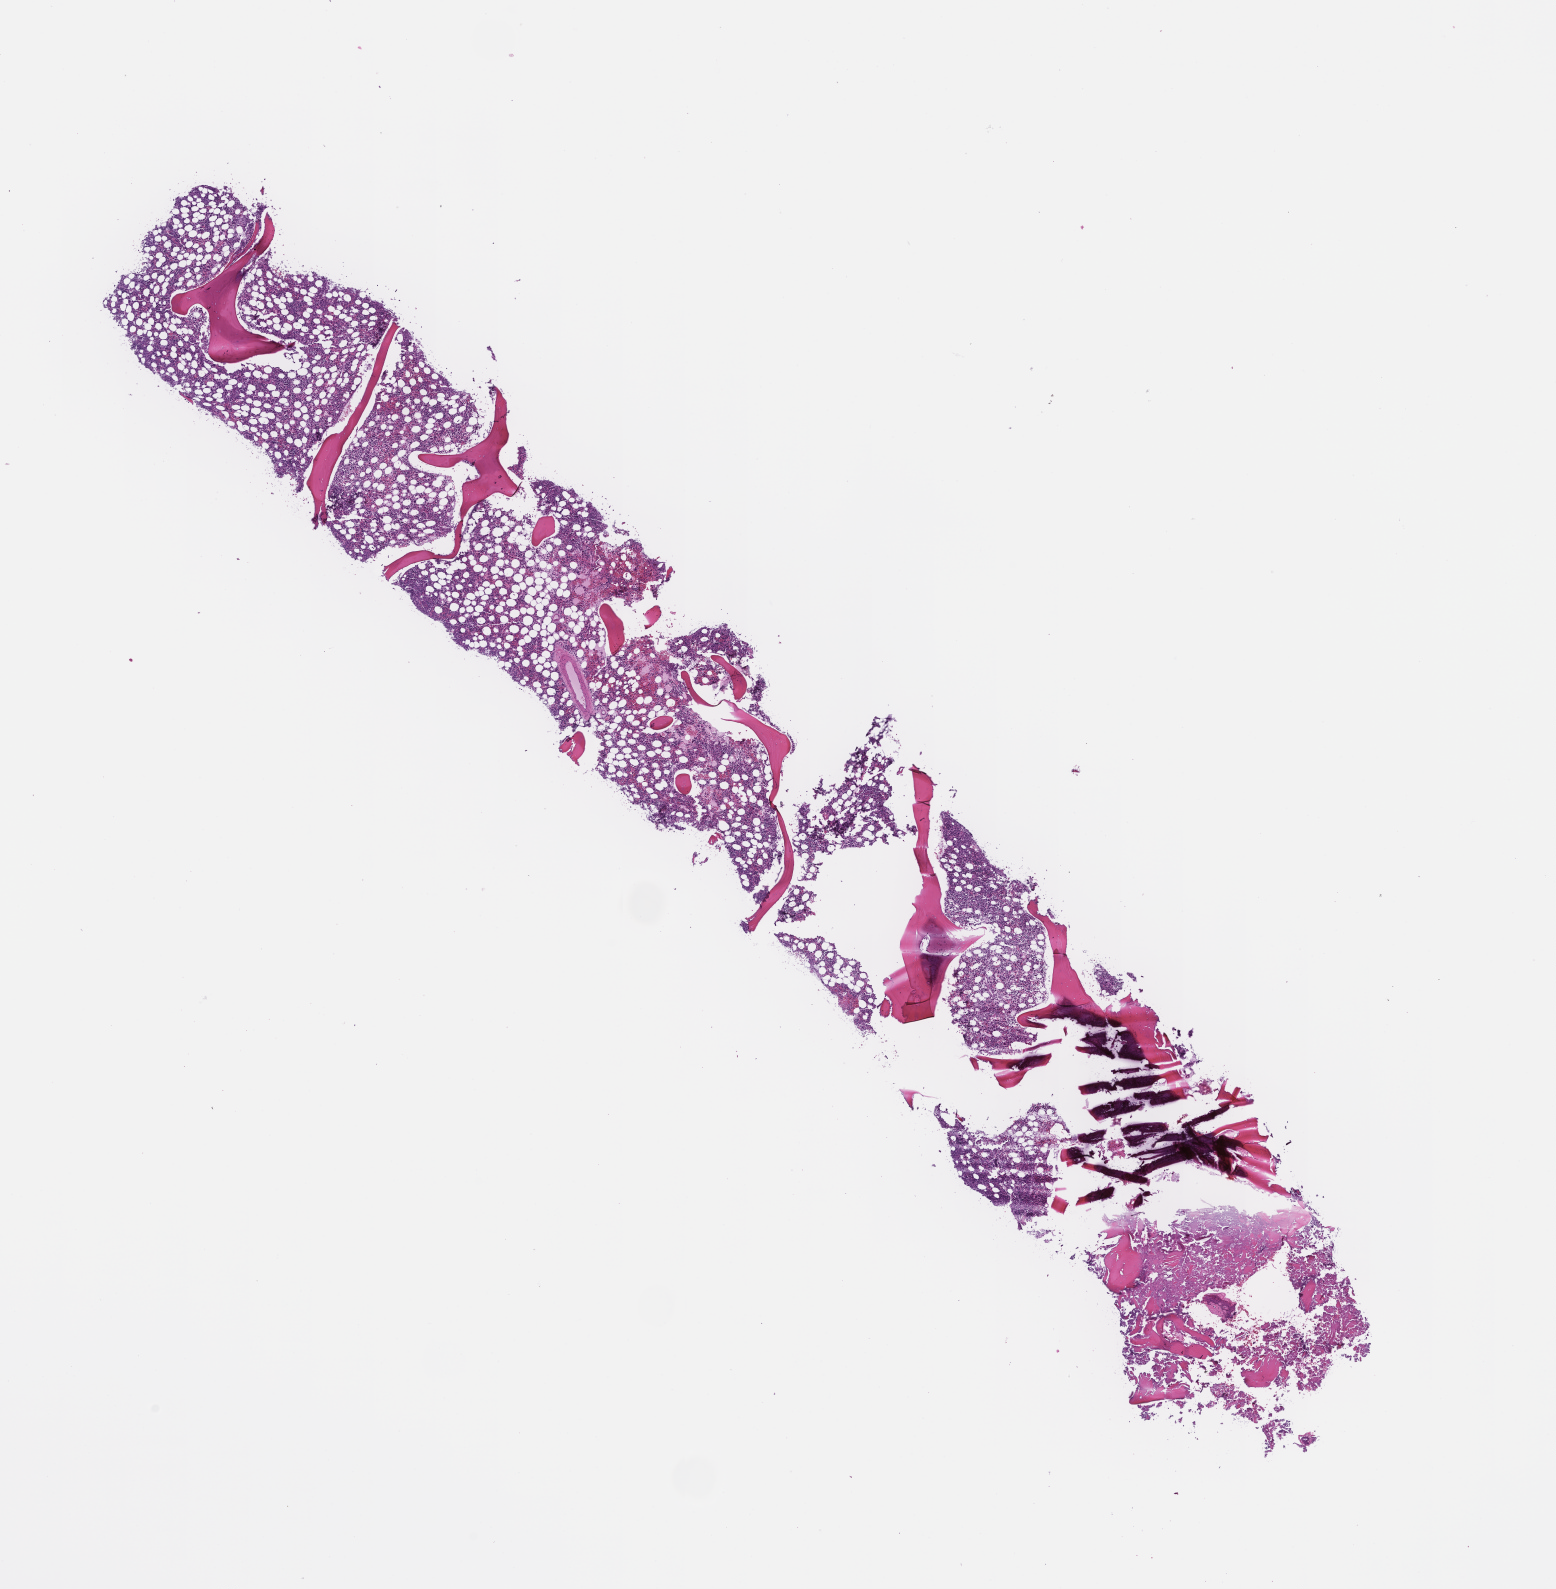
Whole-slide image, hematoxylin and eosin (H&E) stain, a low-resolution overview of the entire scanned area, about 12.6 x 12.8 mm, formalin-fixed, paraffin-embedded (FFPE) tissue, site: bone marrow, specimen time point: archival tissue. Male patient.
From a patient with: Plasma Cell Myeloma.